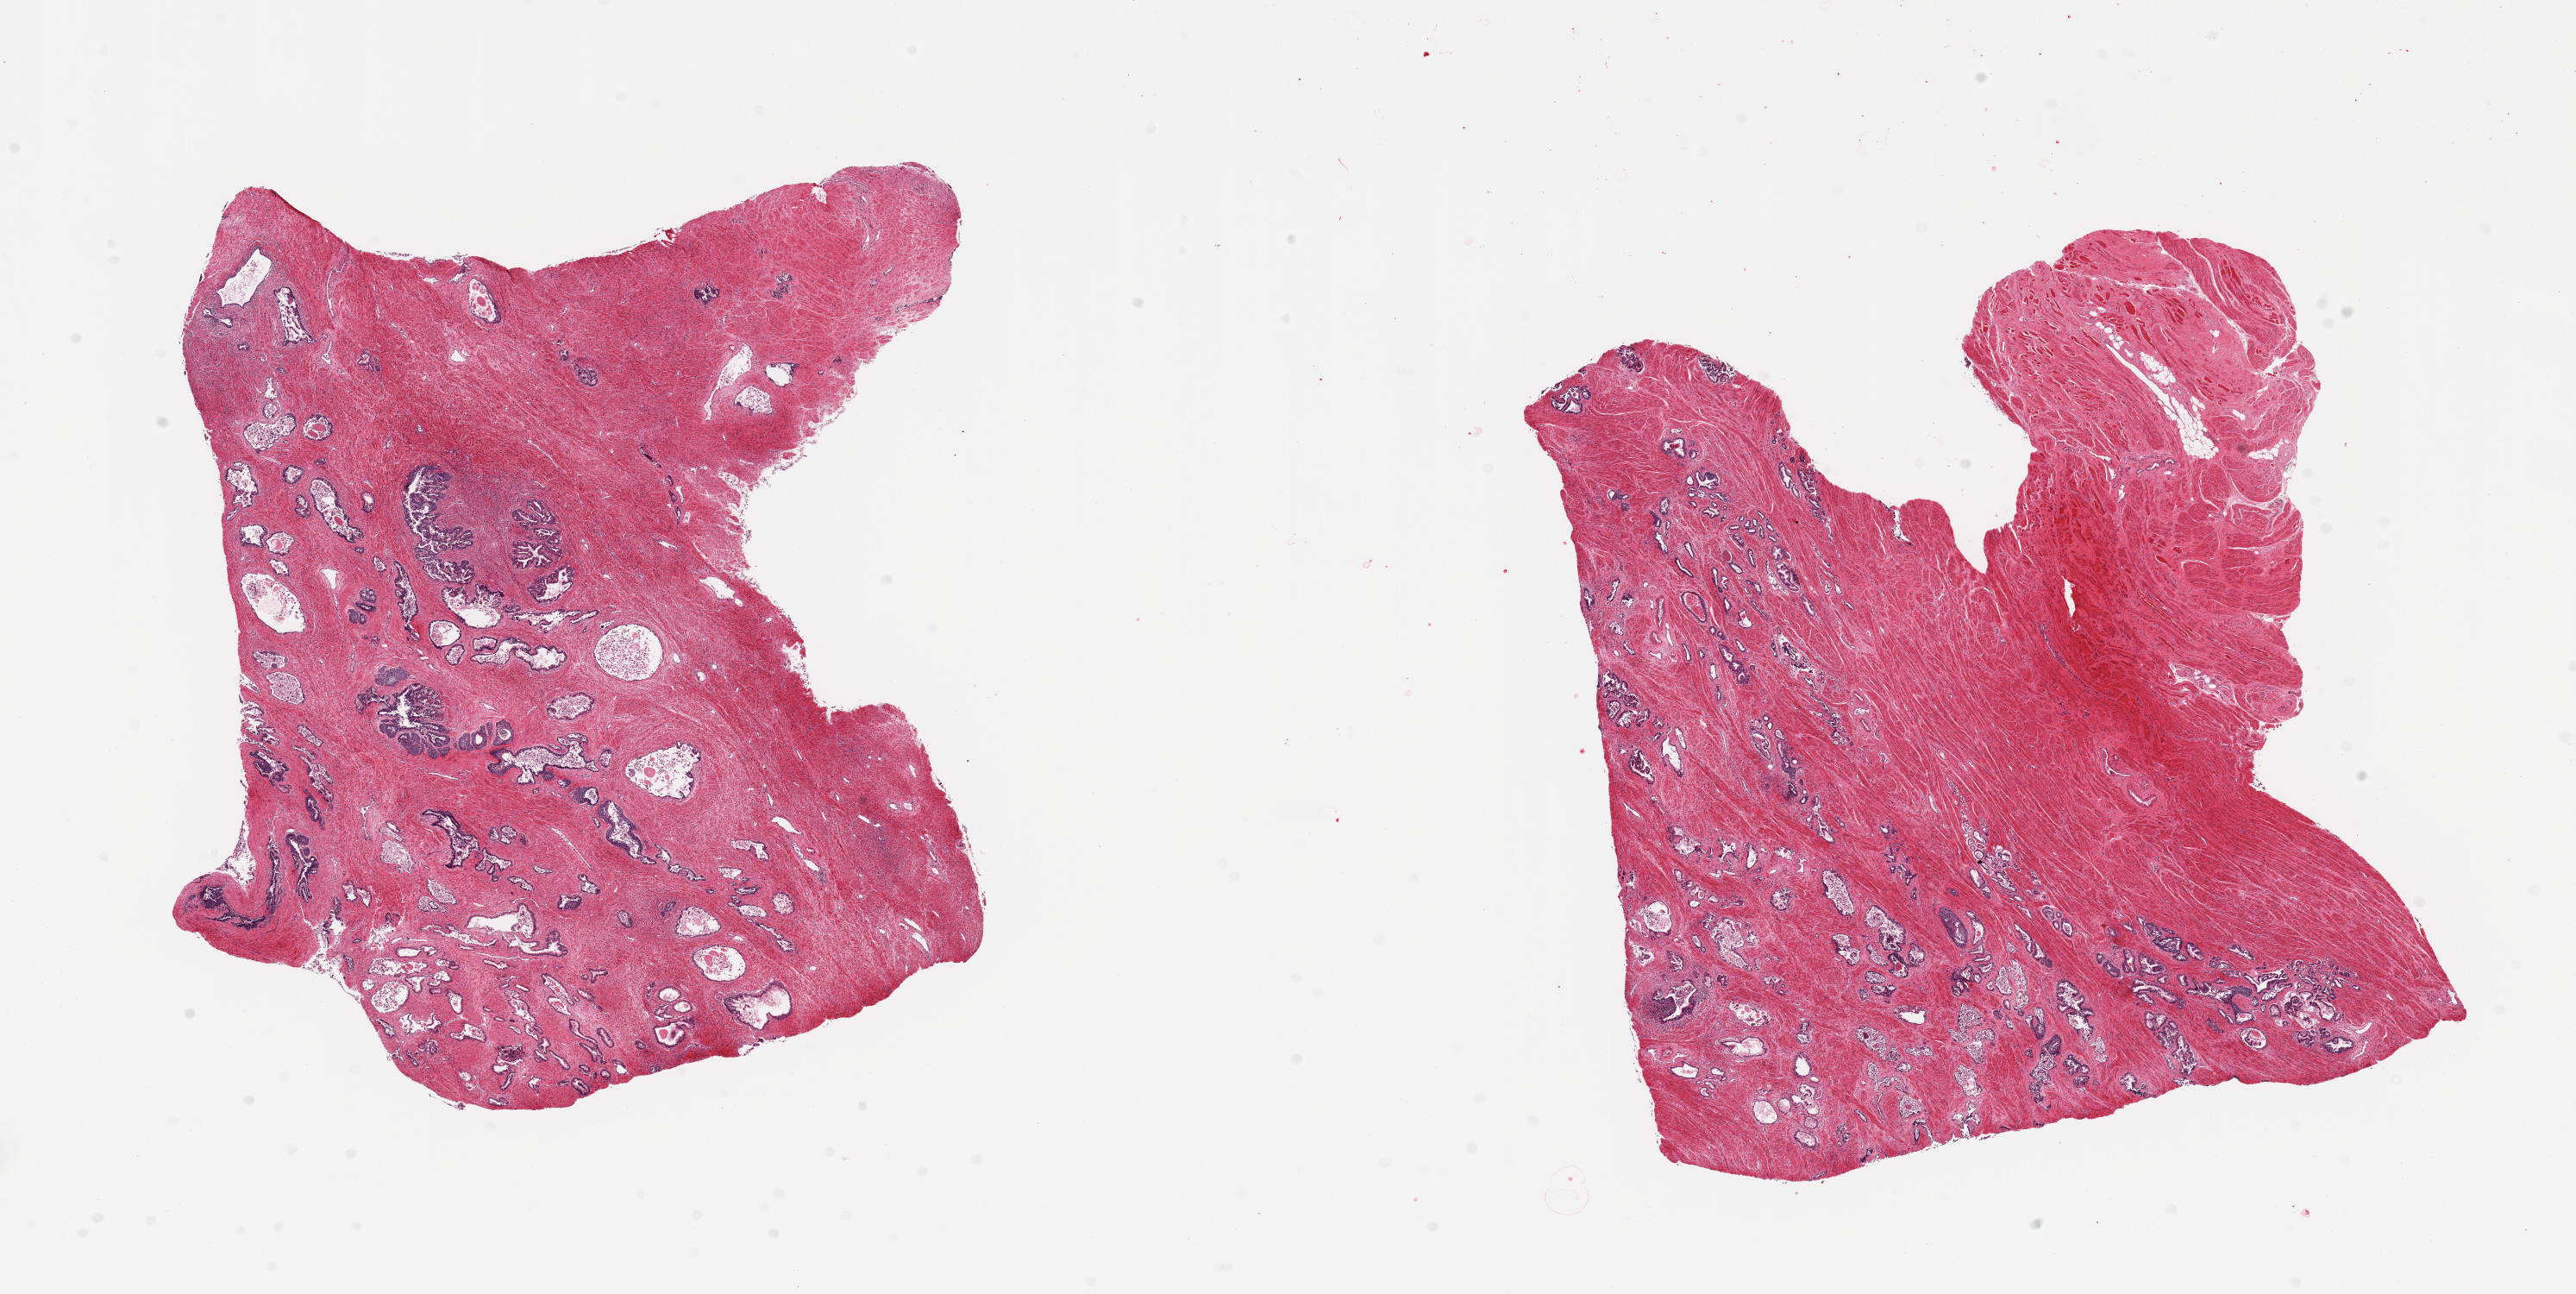
H&E whole-slide image, whole scanned area (about 23.6 x 11.9 mm) shown as a low-resolution overview. PAXgene-fixed, paraffin-embedded tissue. Target tissue: prostate. Donor tissue sample. Male donor.
* review note (as recorded): 2 pieces; stroma in better shape than glands